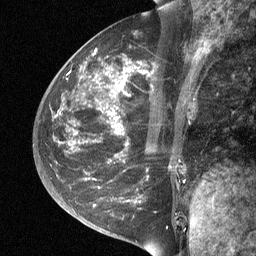
Breast MRI (dynamic contrast-enhanced), one sagittal slice. Slice 25 of 64 in the series (ordered by position). Dynamic contrast-enhanced study with each time point stored as its own series, time point 2 of 3 at this slice position (early post-contrast, ordered by acquisition time). 1.5 T. TE 4.8 ms, TR 27 ms. 2 mm slice thickness. 256 × 256 image matrix, field of view 200 × 200 mm. Female patient, age 42 years. Case-level facts recorded for this patient, not image findings: setting: breast cancer imaged before/during neoadjuvant chemotherapy; receptor status: triple-negative.
Structures marked on this image (semi-automatic segmentation, software-assisted and operator-edited):
- analysis volume of interest (the breast-tissue region the enhancement analysis was run in; not a lesion): bounding box [x1, y1, x2, y2] px = [49, 45, 199, 197]
- tumour enhancement mask (voxels above the 90 % enhancement threshold inside the analysis volume of interest): [121, 83, 123, 85]